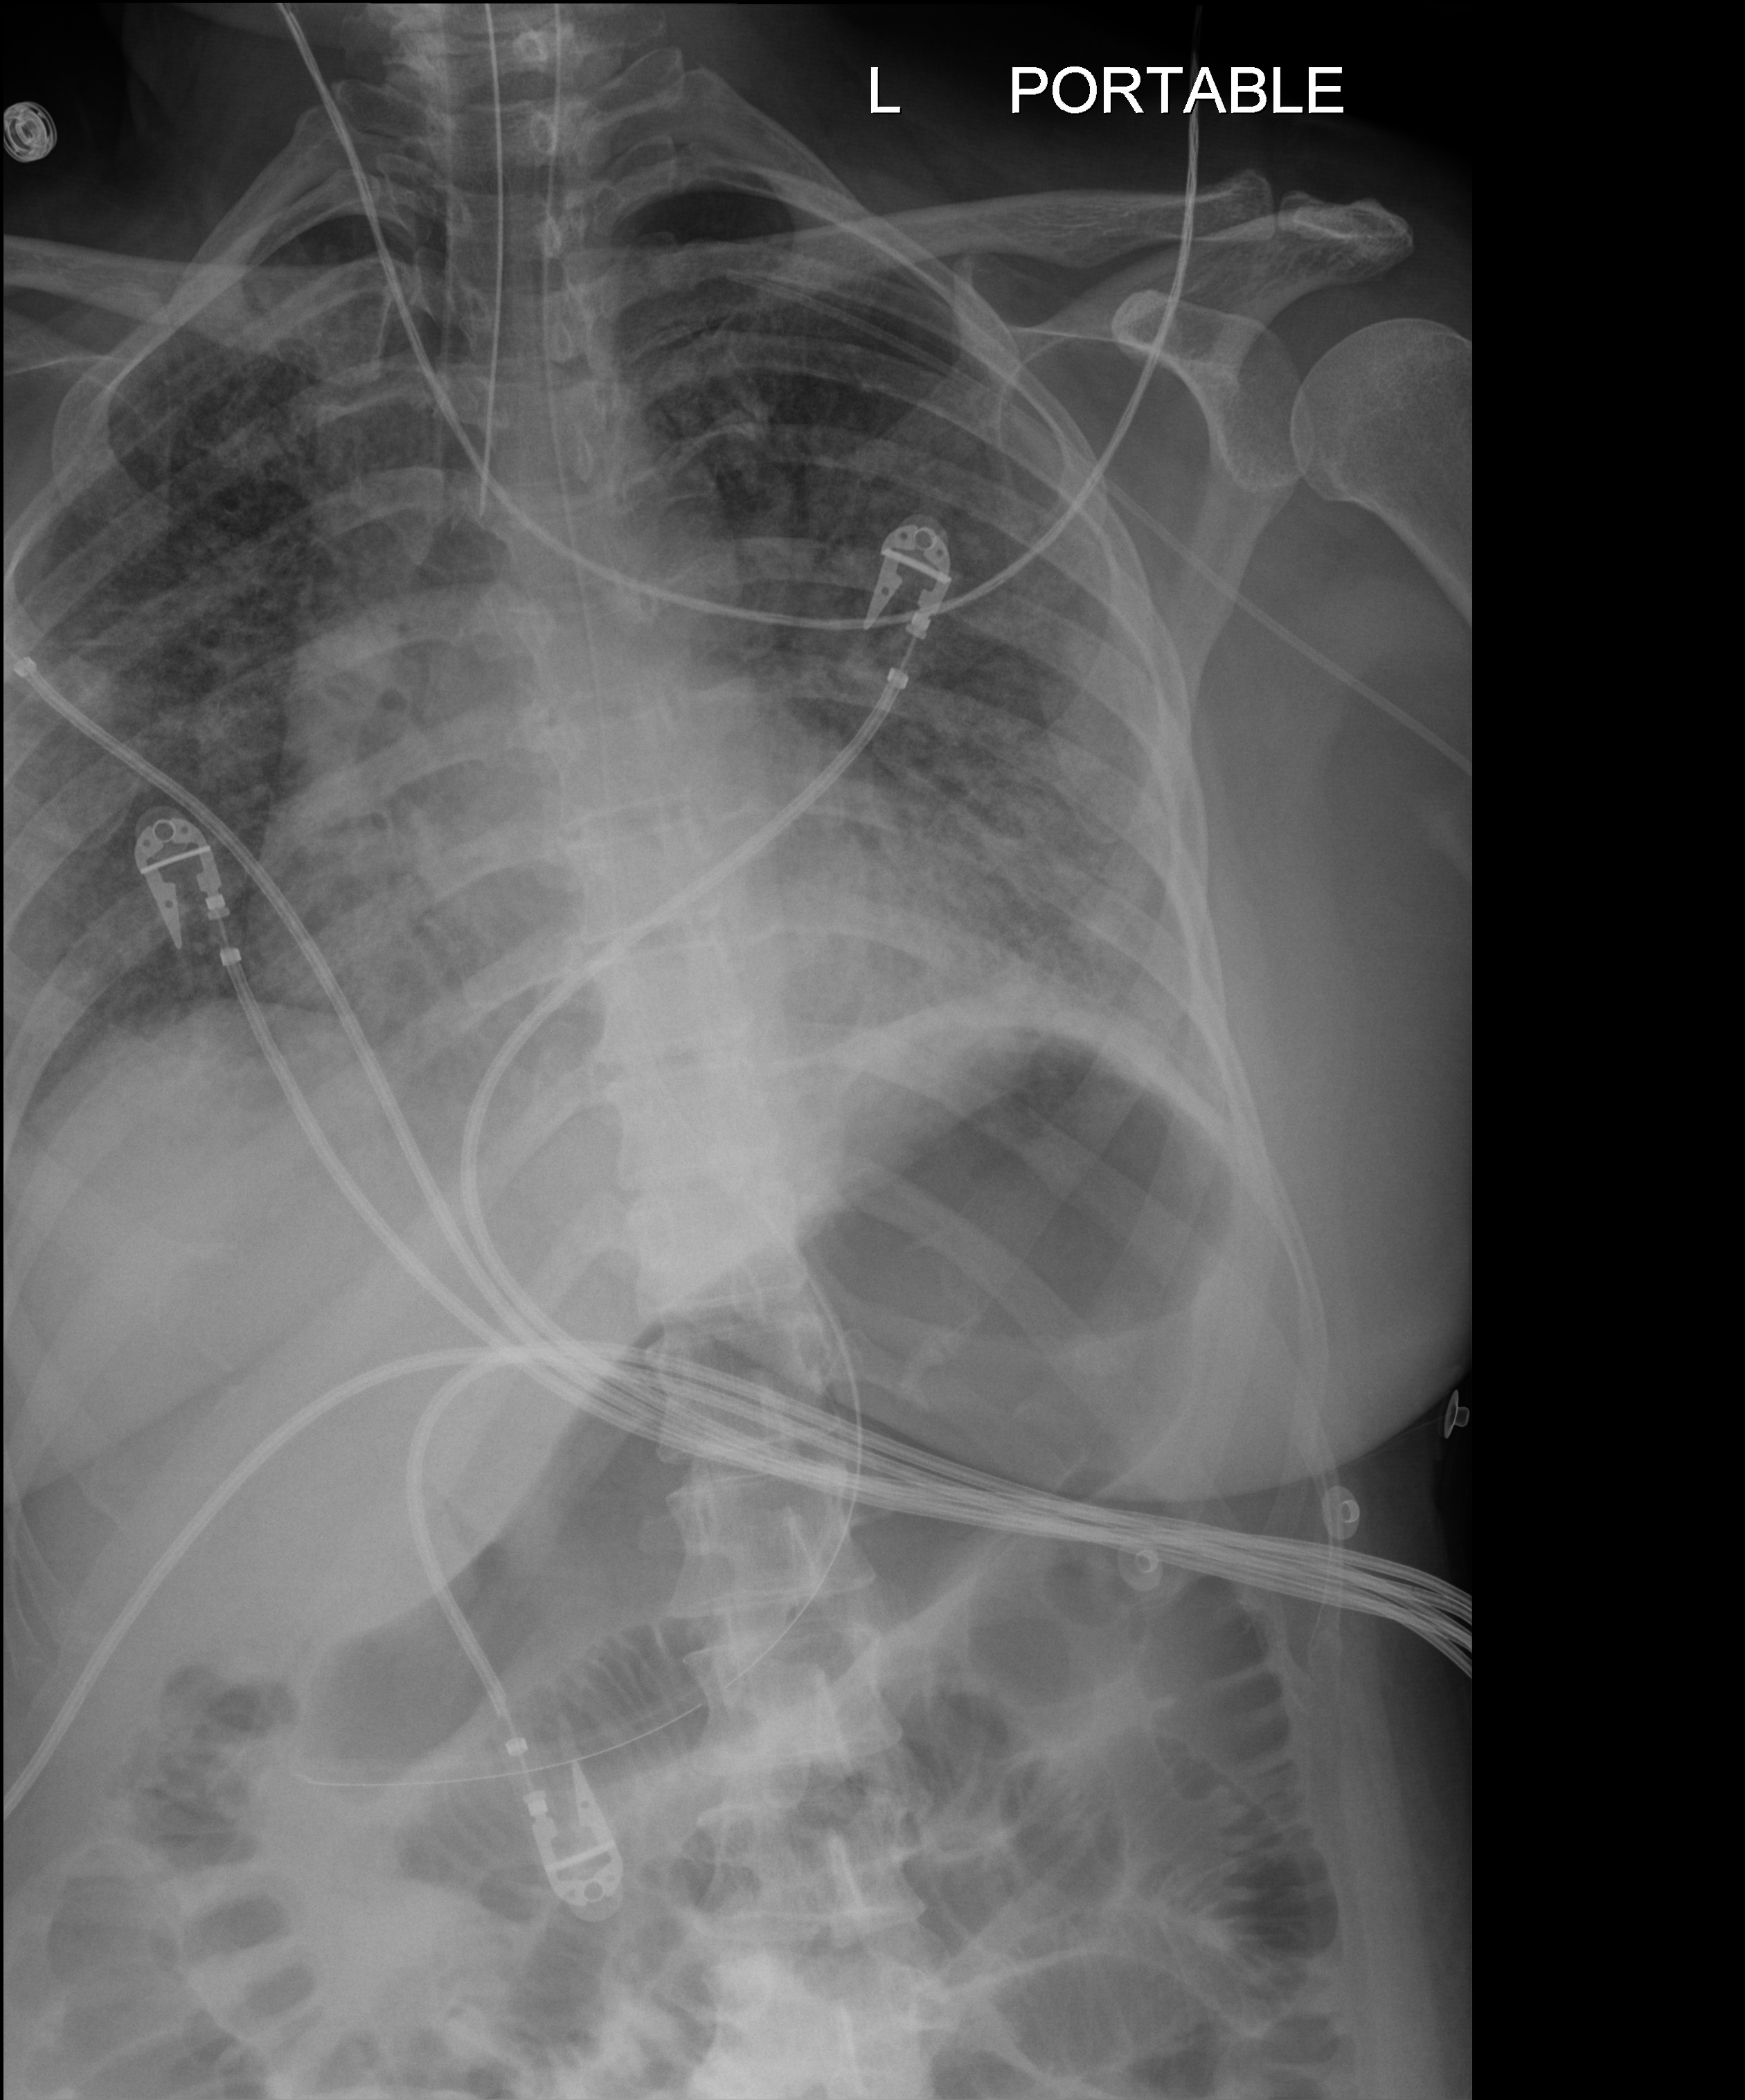
Chest X-ray (portable); anteroposterior (AP) projection. Patient hospitalised with COVID-19; male, aged 18–59 years.
Admission-level facts for this patient (not findings on this image; timing relative to this image not recorded):
- COPD (admission record): no